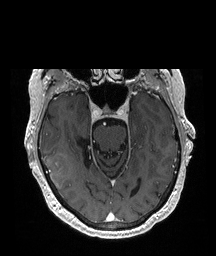
Brain MRI from a brain-tumour surgery series, one axial slice. Slice 135 of 208 in the series (ordered by position). T1-weighted post-contrast. 216 × 256 image matrix, field of view 216 × 256 mm. From the clinical record (not read from this slice): histopathology: Glioblastoma; WHO grade: 4; IDH mutation: no.
Outlined on this slice (outlined manually by an expert reader):
- tumour: box from (x=45, y=153) to (x=73, y=189) px